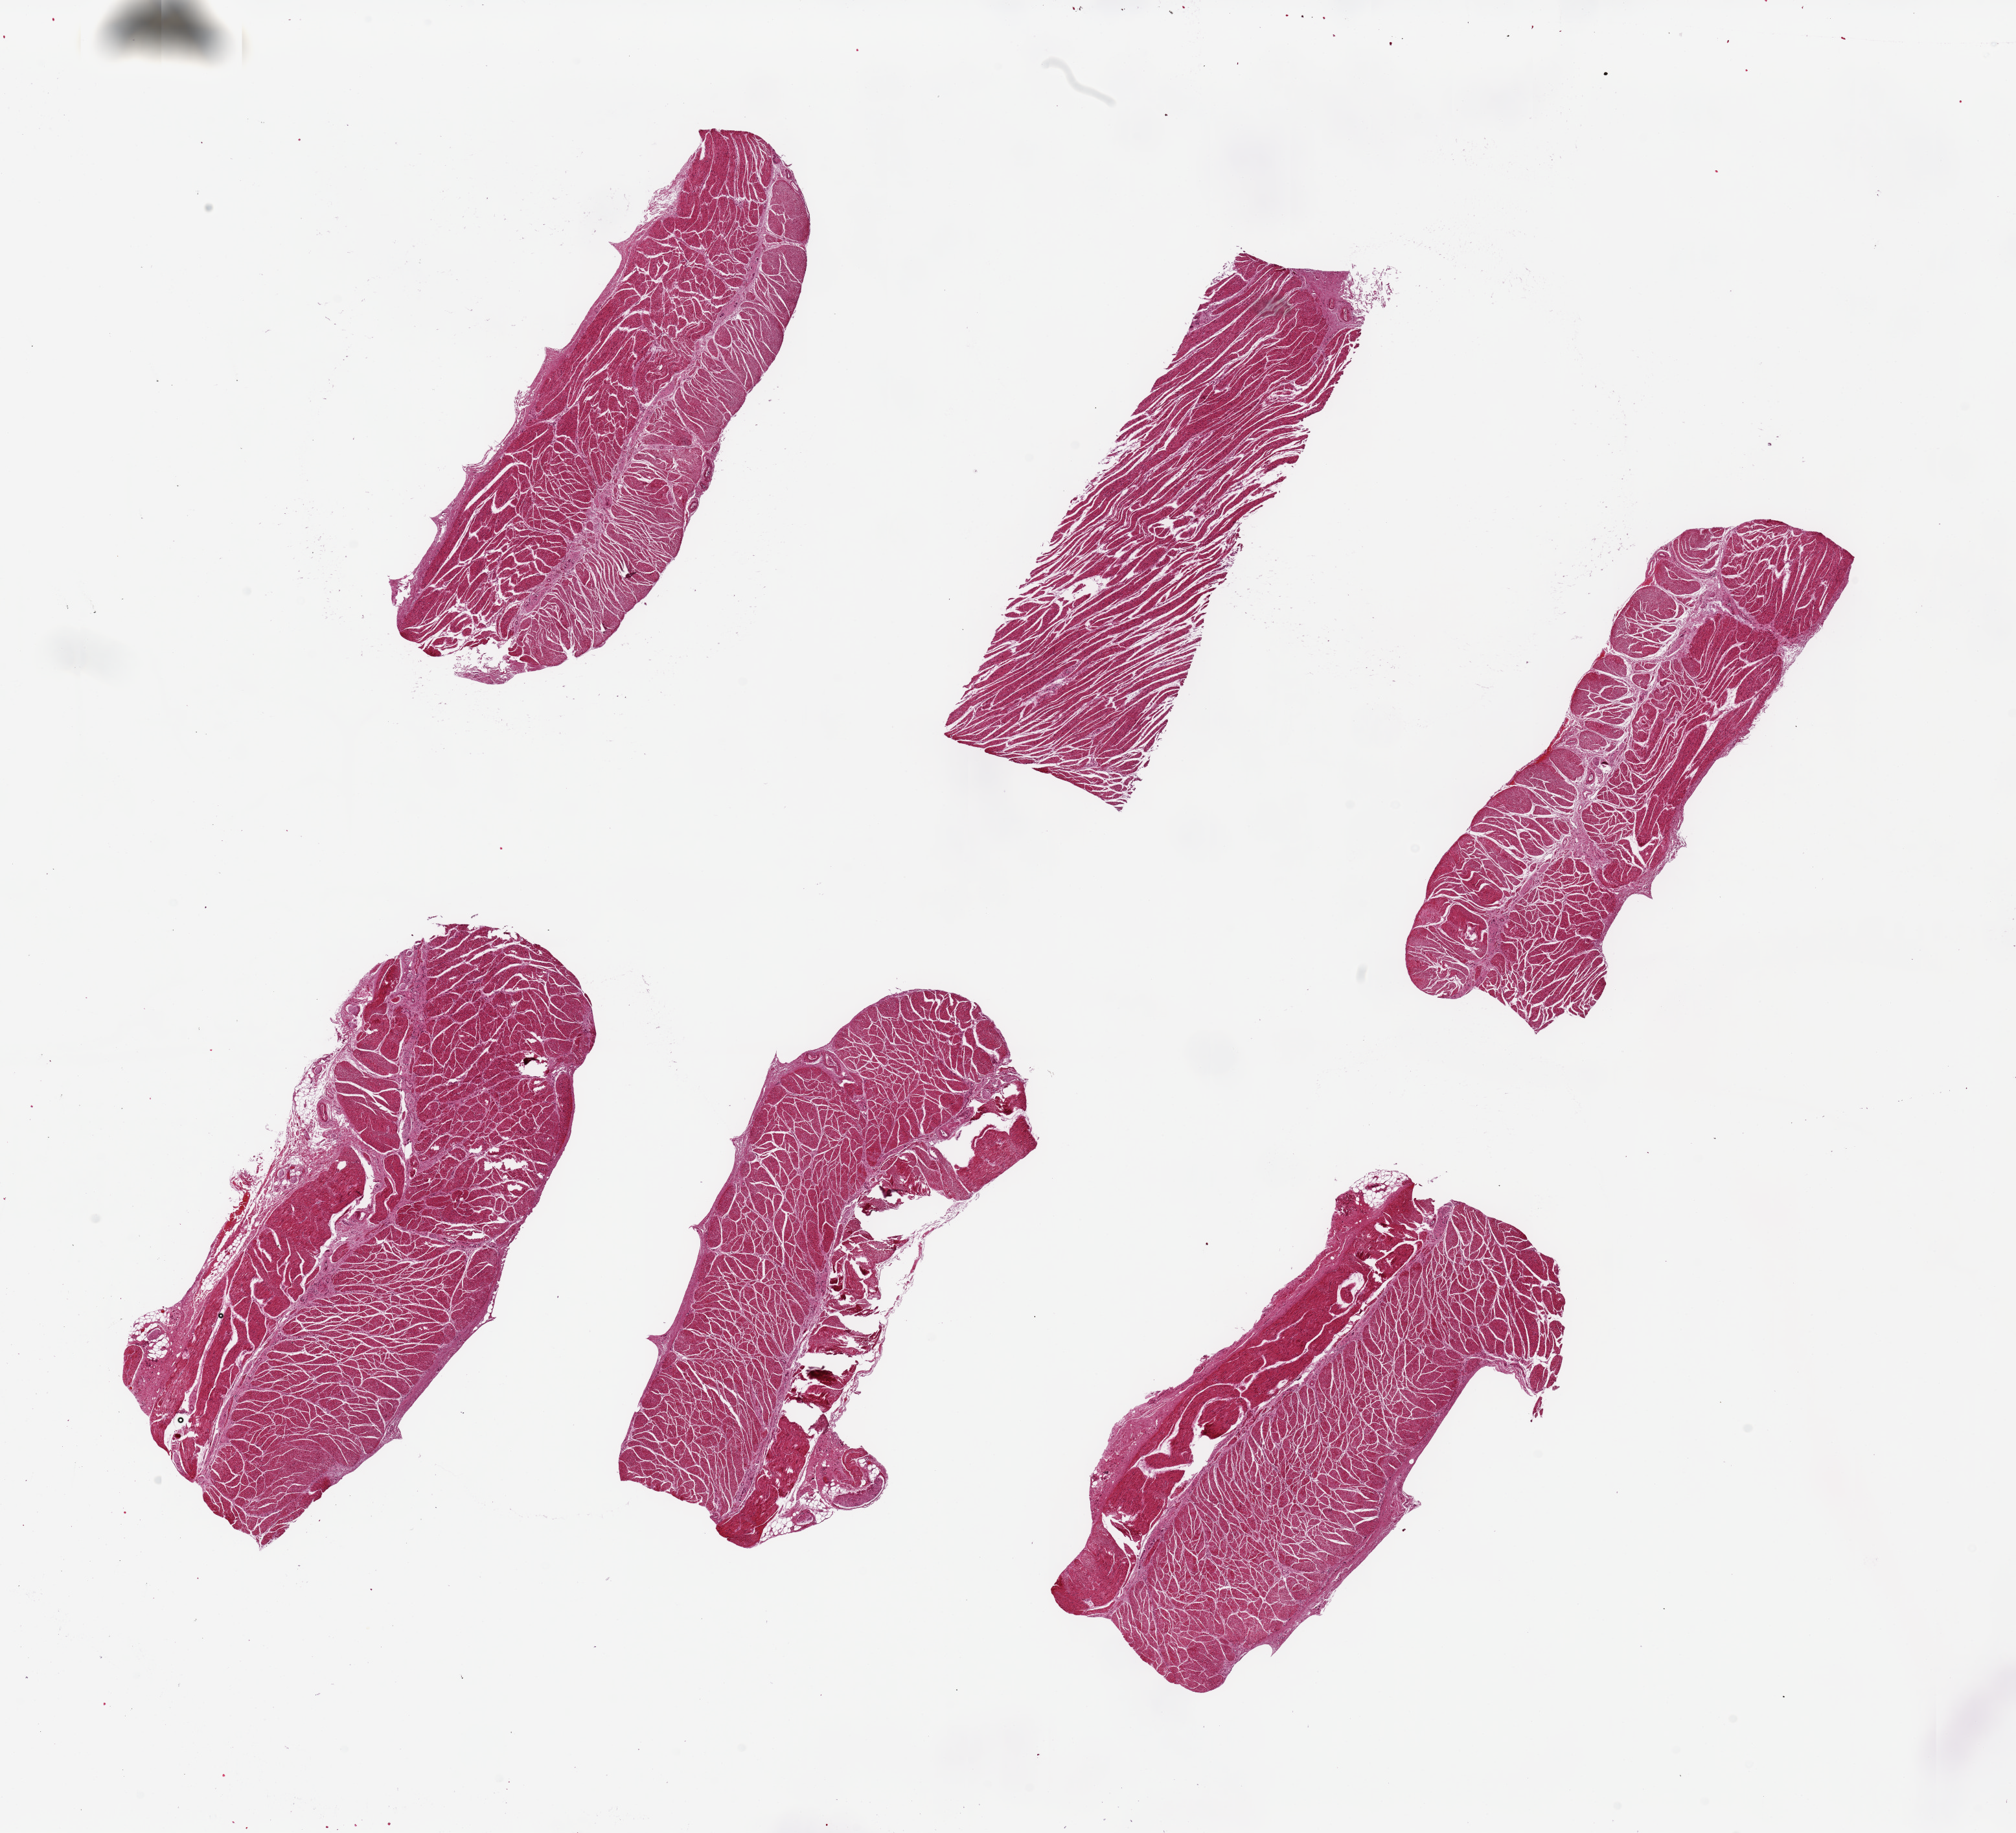
Haematoxylin and eosin whole-slide image, a low-resolution overview of the entire scanned area, about 24.6 x 22.4 mm (acquisition: 20x scan), PAXgene-fixed, paraffin-embedded tissue, target tissue: esophageal muscle, donor tissue sample. Donor: female.
Pathologist's review note for this sample: 6 pieces, up to 8x3mm; muscle show loss of cohesion.